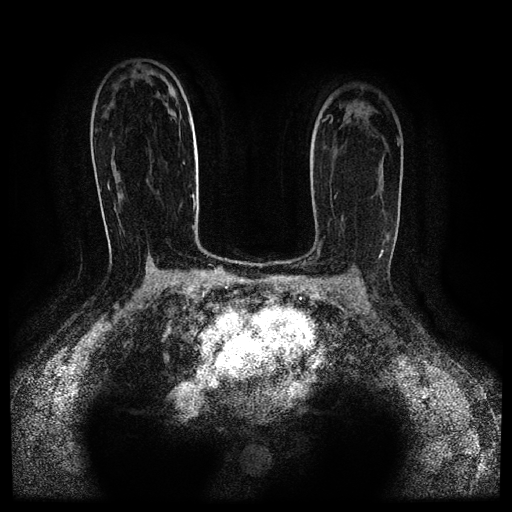
Breast MRI (dynamic contrast-enhanced, multi-phase), one axial slice; position 63 of 116 along the scan axis; dynamic contrast-enhanced series, time point 2 of 5 at this slice position (early post-contrast); 1.5 T; TE 2.6 ms, TR 5.3 ms; 2 mm slice thickness; 512 × 512 image matrix, field of view 350 × 350 mm. Patient: female, 52 years.
Outlined on this slice (semi-automatically segmented with operator editing):
- breast lesion (labelled benign in the annotation): bounding box (x1, y1, x2, y2) in pixels: (170, 89, 172, 93)